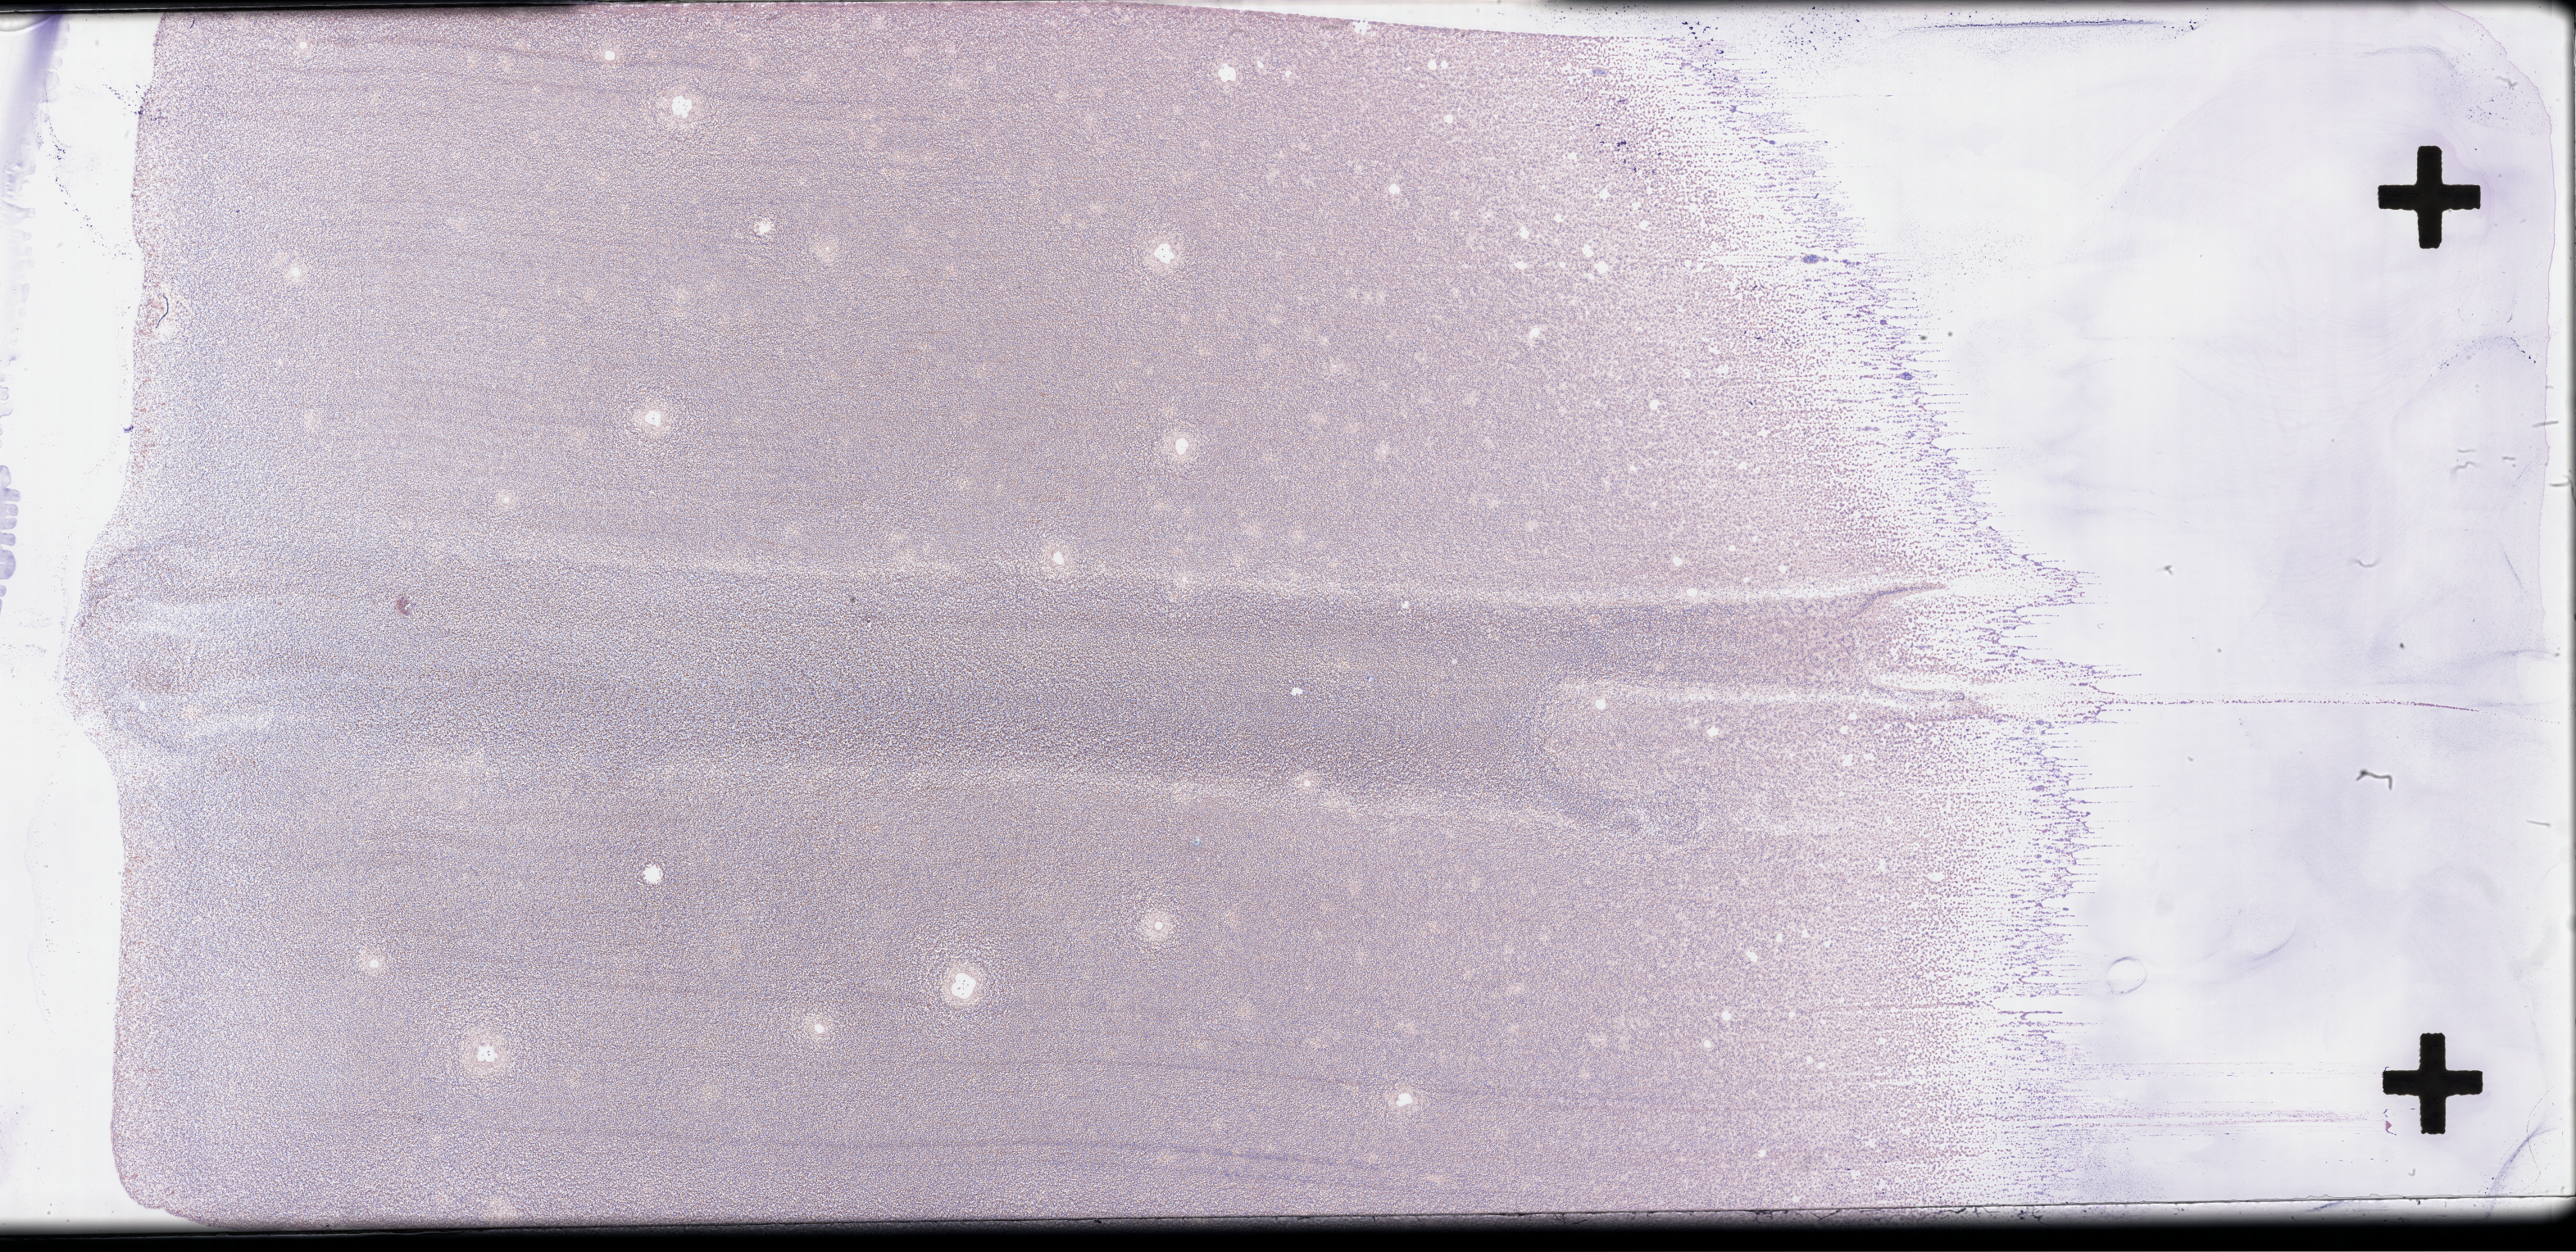
Wright-Giemsa-stained bone marrow smear, whole-slide image — low-resolution overview of the scanned area, about 50.8 x 24.7 mm. Smear from an EDTA sample. Collected at baseline (before treatment). Patient: female.
• from a patient with: Acute Myeloid Leukemia Not Otherwise Specified